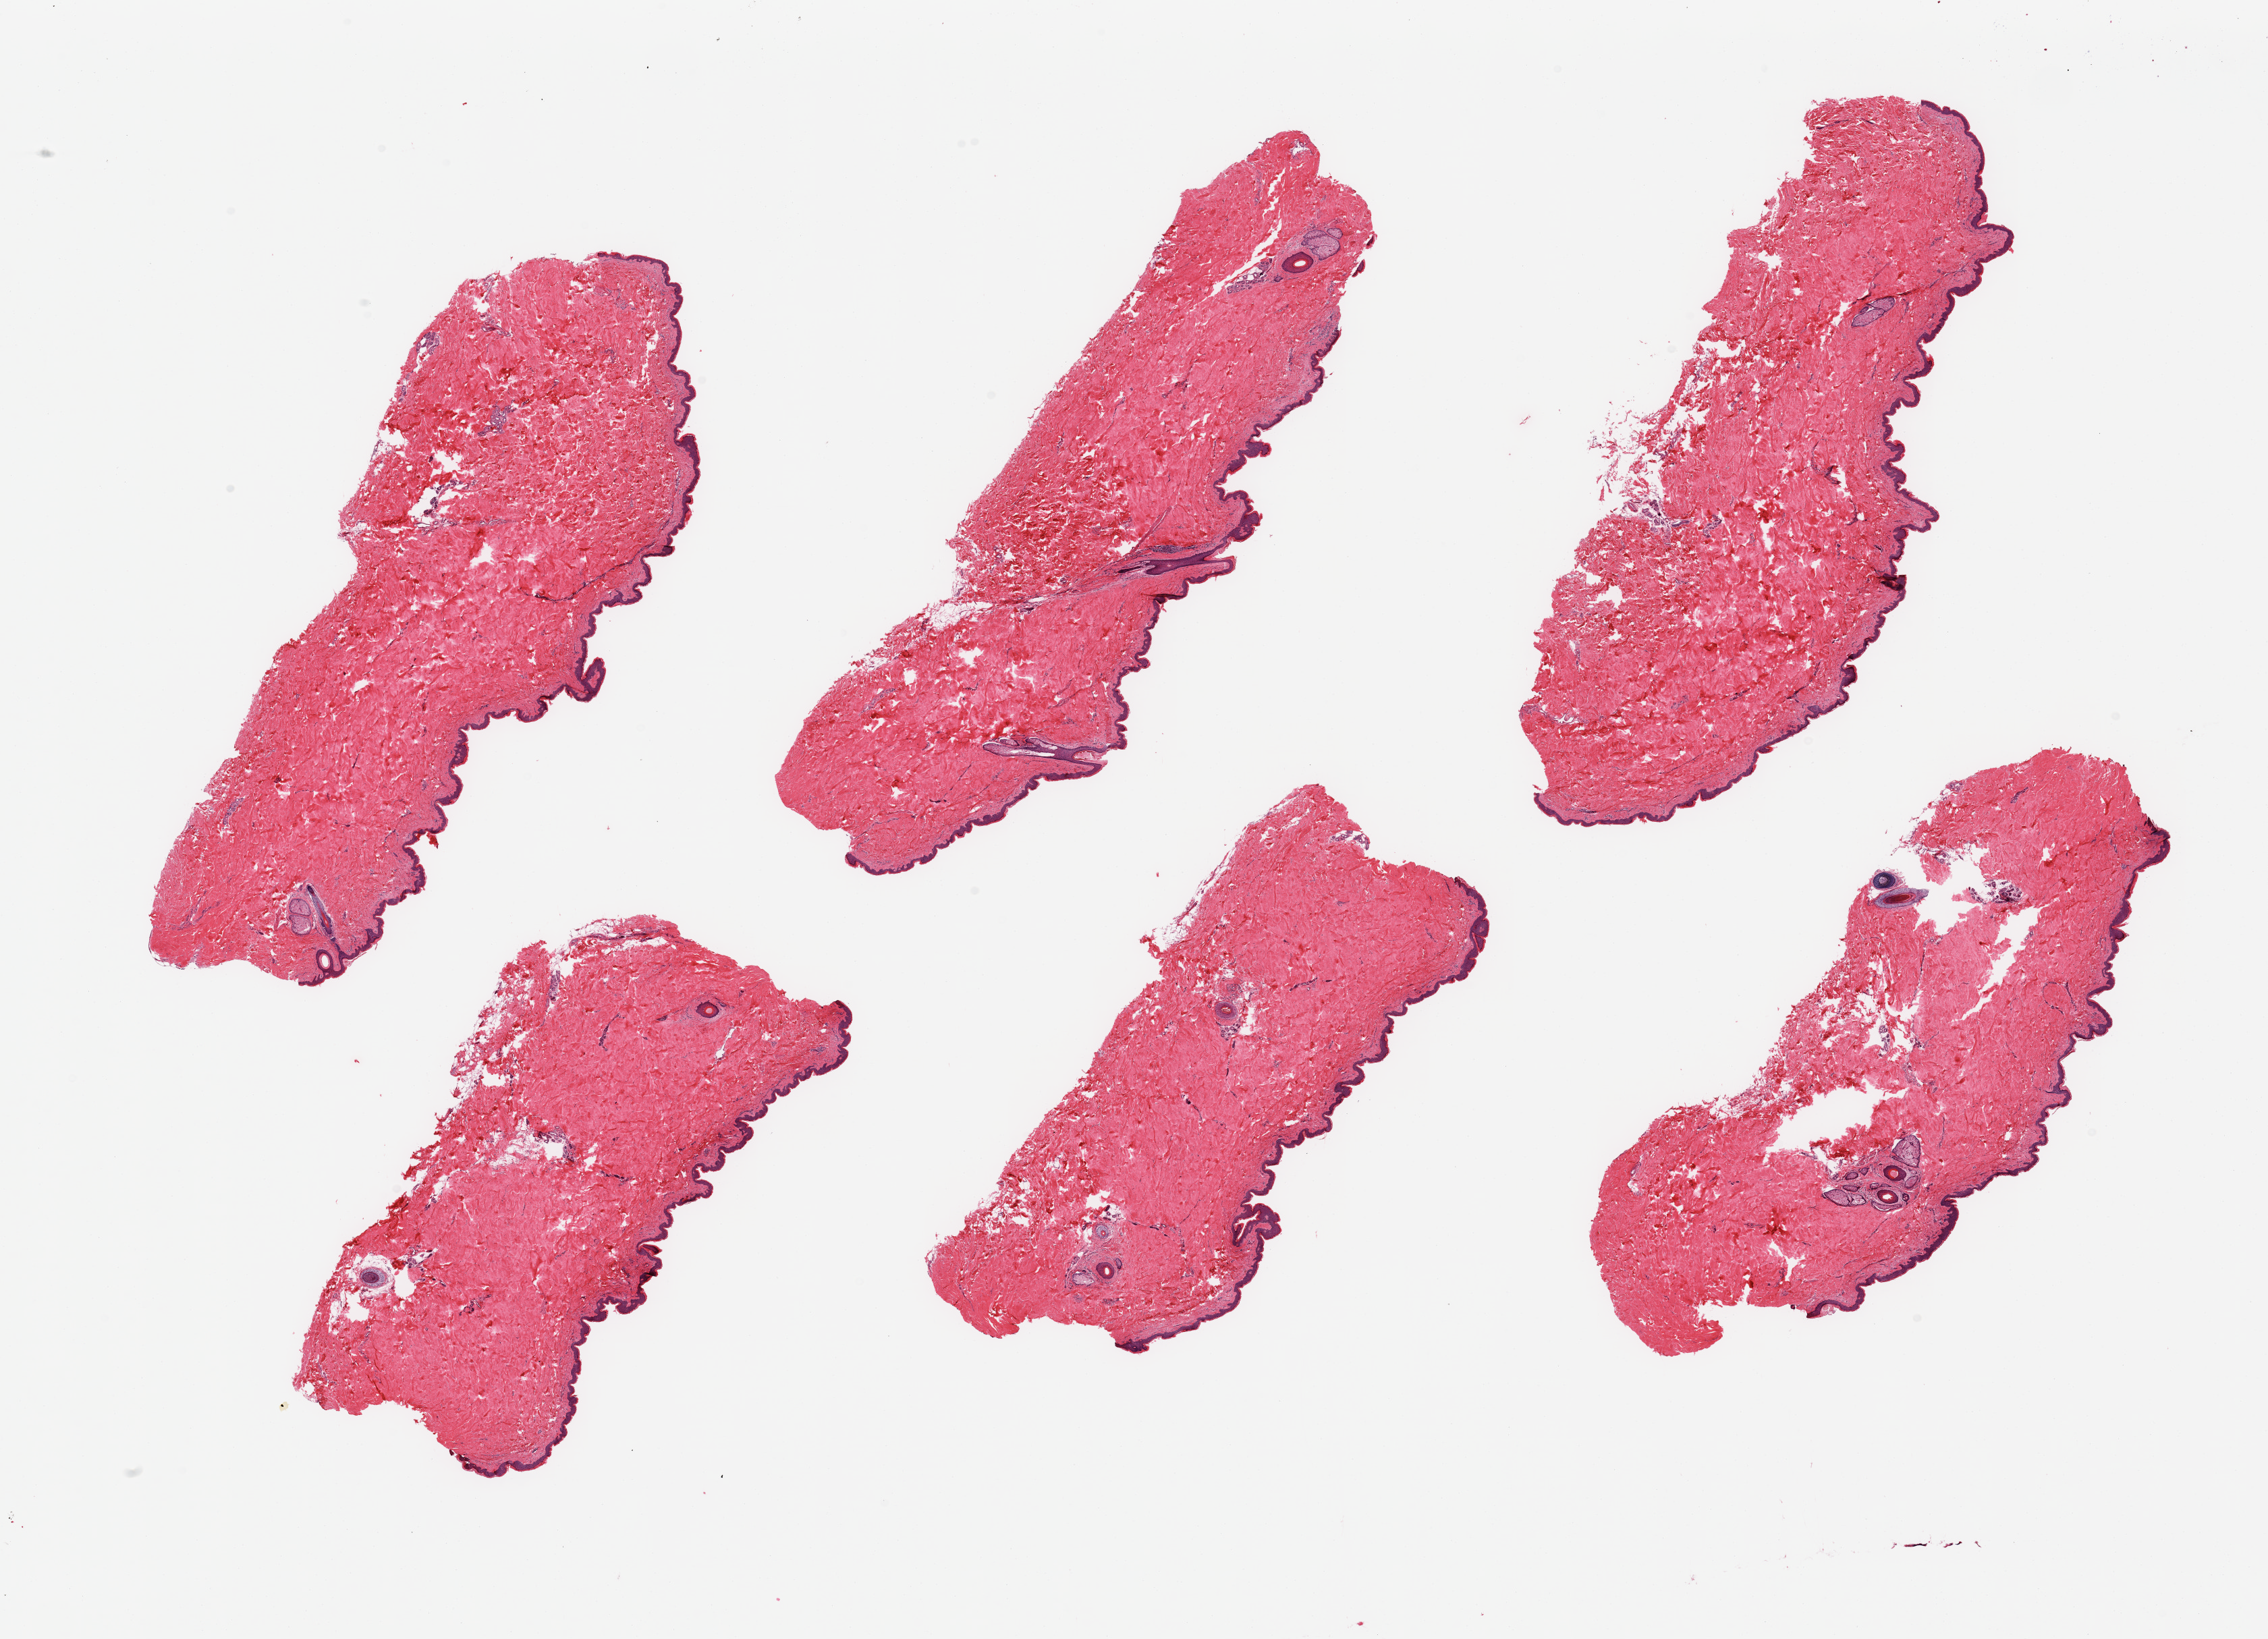
Whole-slide image, hematoxylin and eosin (H&E) stain, whole scanned area (about 26.6 x 19.2 mm) shown as a low-resolution overview. PAXgene-fixed, paraffin-embedded tissue. Section of skin of suprapubic region (target tissue). Donor tissue sample.
Pathologist's review note for this sample: 6 pieces, Squamous epithelium is ~40-50 microns; no dermal fat.